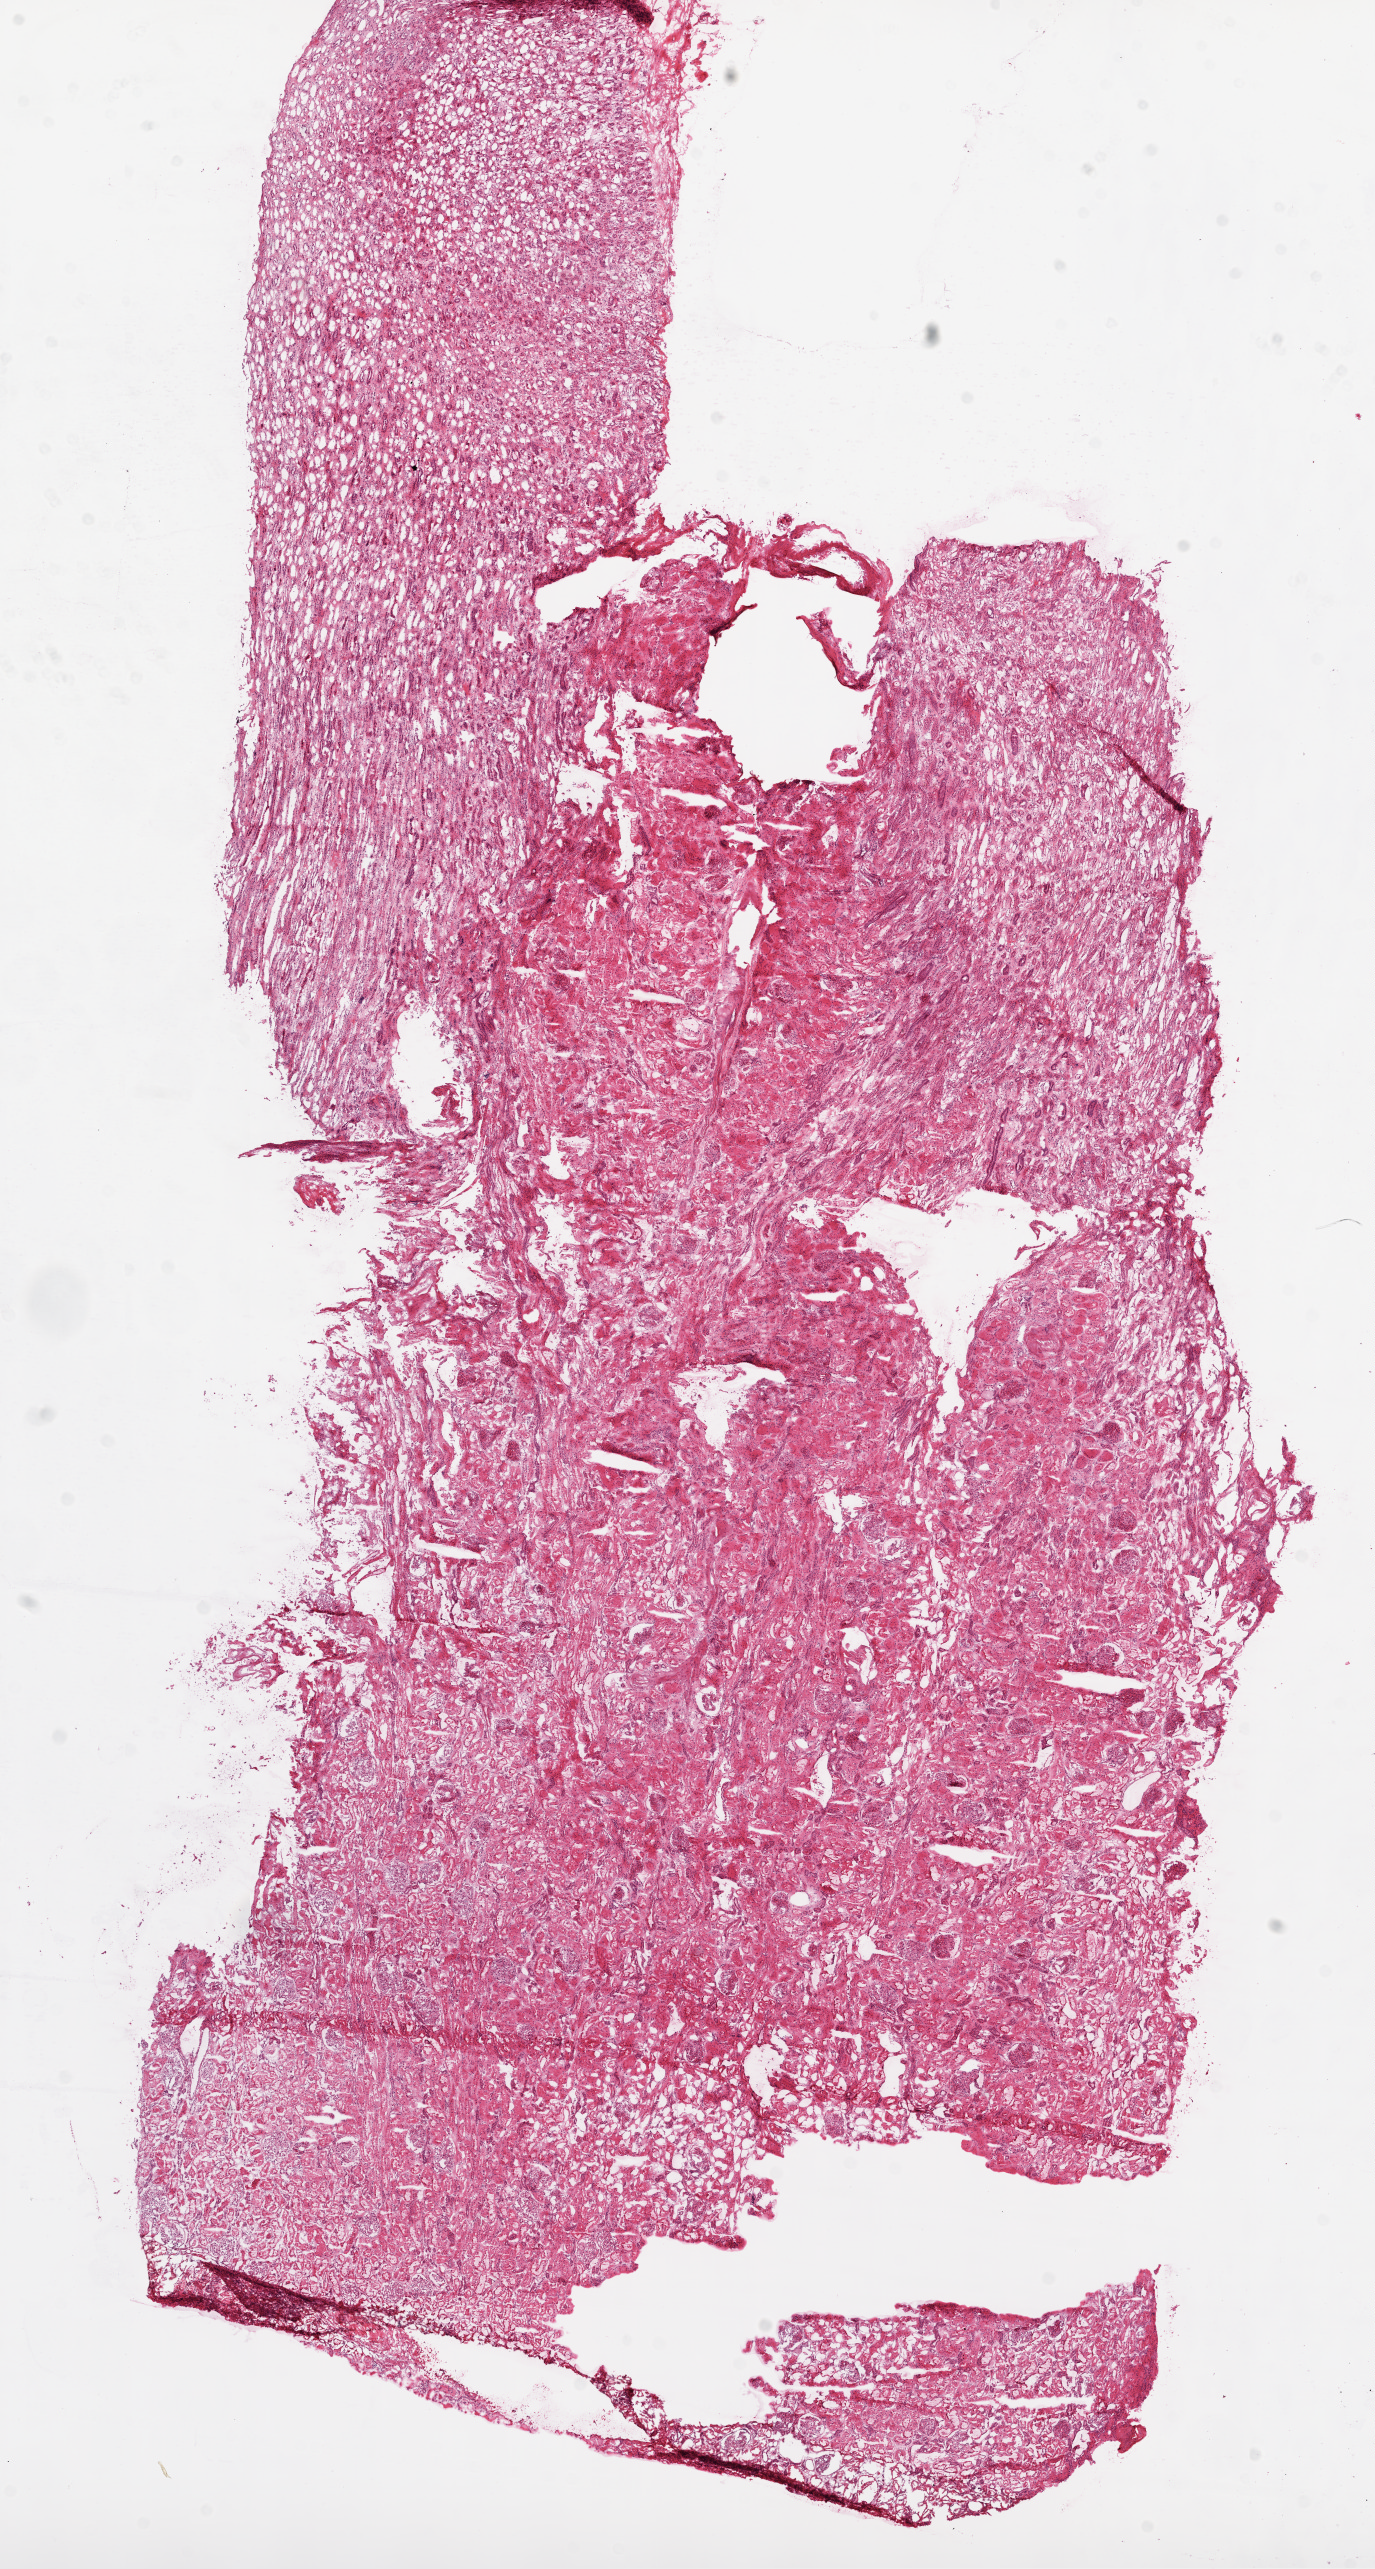
Hematoxylin and eosin (H&E) stained whole-slide image, whole scanned area (about 11.0 x 20.6 mm, from a 20x scan) shown as a low-resolution overview, frozen section from the top of the tissue portion, sample: solid tissue normal (non-tumour tissue), kidney. Patient: female, age at initial diagnosis 53 years.
This section: solid tissue normal (non-tumour) sample from the same patient. Patient diagnosis: Clear cell adenocarcinoma, NOS.